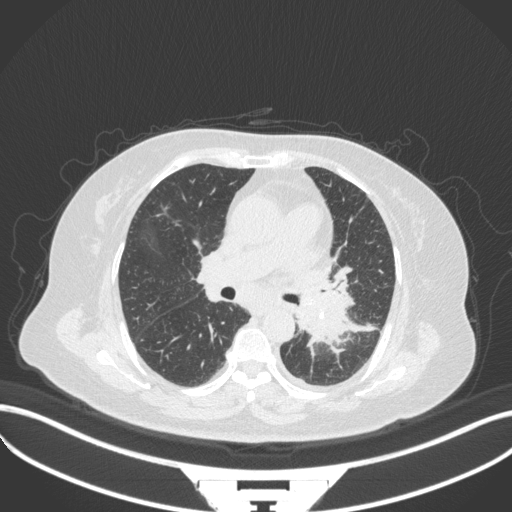
Chest CT, one axial slice. Slice 196 of 328 in the series (ordered by position). Reconstruction kernel B31f. 120 kVp. Lung window (W 1500 / L -600 HU). 1 mm slice thickness. 512 × 512 image matrix, field of view 400 × 400 mm. Patient: female, 69 years. From the clinical record (not read from this slice): clinical TNM (as recorded): T2b N3 M1.
Structures marked on this image (bounding box drawn by a radiologist):
- lung tumour (recorded histology: adenocarcinoma): bounding box [x1, y1, x2, y2] px = [290, 279, 359, 348]